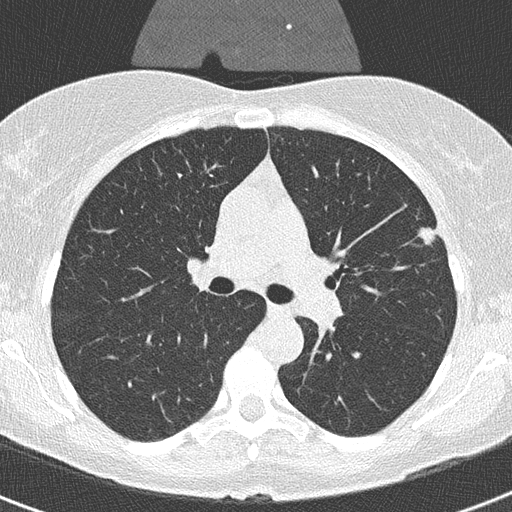
Low-dose screening chest CT, axial slice; second screening round (one year after baseline); lung window (W 1500 / L -600 HU); 2 mm slice thickness; lung (sharp) reconstruction kernel (B50f); slice 111 of 320 in the series. Female, age 56 years at enrolment. Former smoker at enrolment.
Expert reader's lesion annotation, box from (x=404, y=201) to (x=454, y=255) px. Reader record for this screening exam (exam-level; its link to the box is not recorded): non-calcified nodule or mass ≥4 mm, left upper lobe, 20 × 9 mm, smooth margins, soft tissue attenuation, pre-existing on the prior screen: yes; interval growth: yes. Participant outcome: lung cancer diagnosed 55 days after this screen — adenocarcinoma, NOS, left upper lobe, moderately differentiated (G2), stage IA (AJCC 6th edition), 11 mm at pathology.